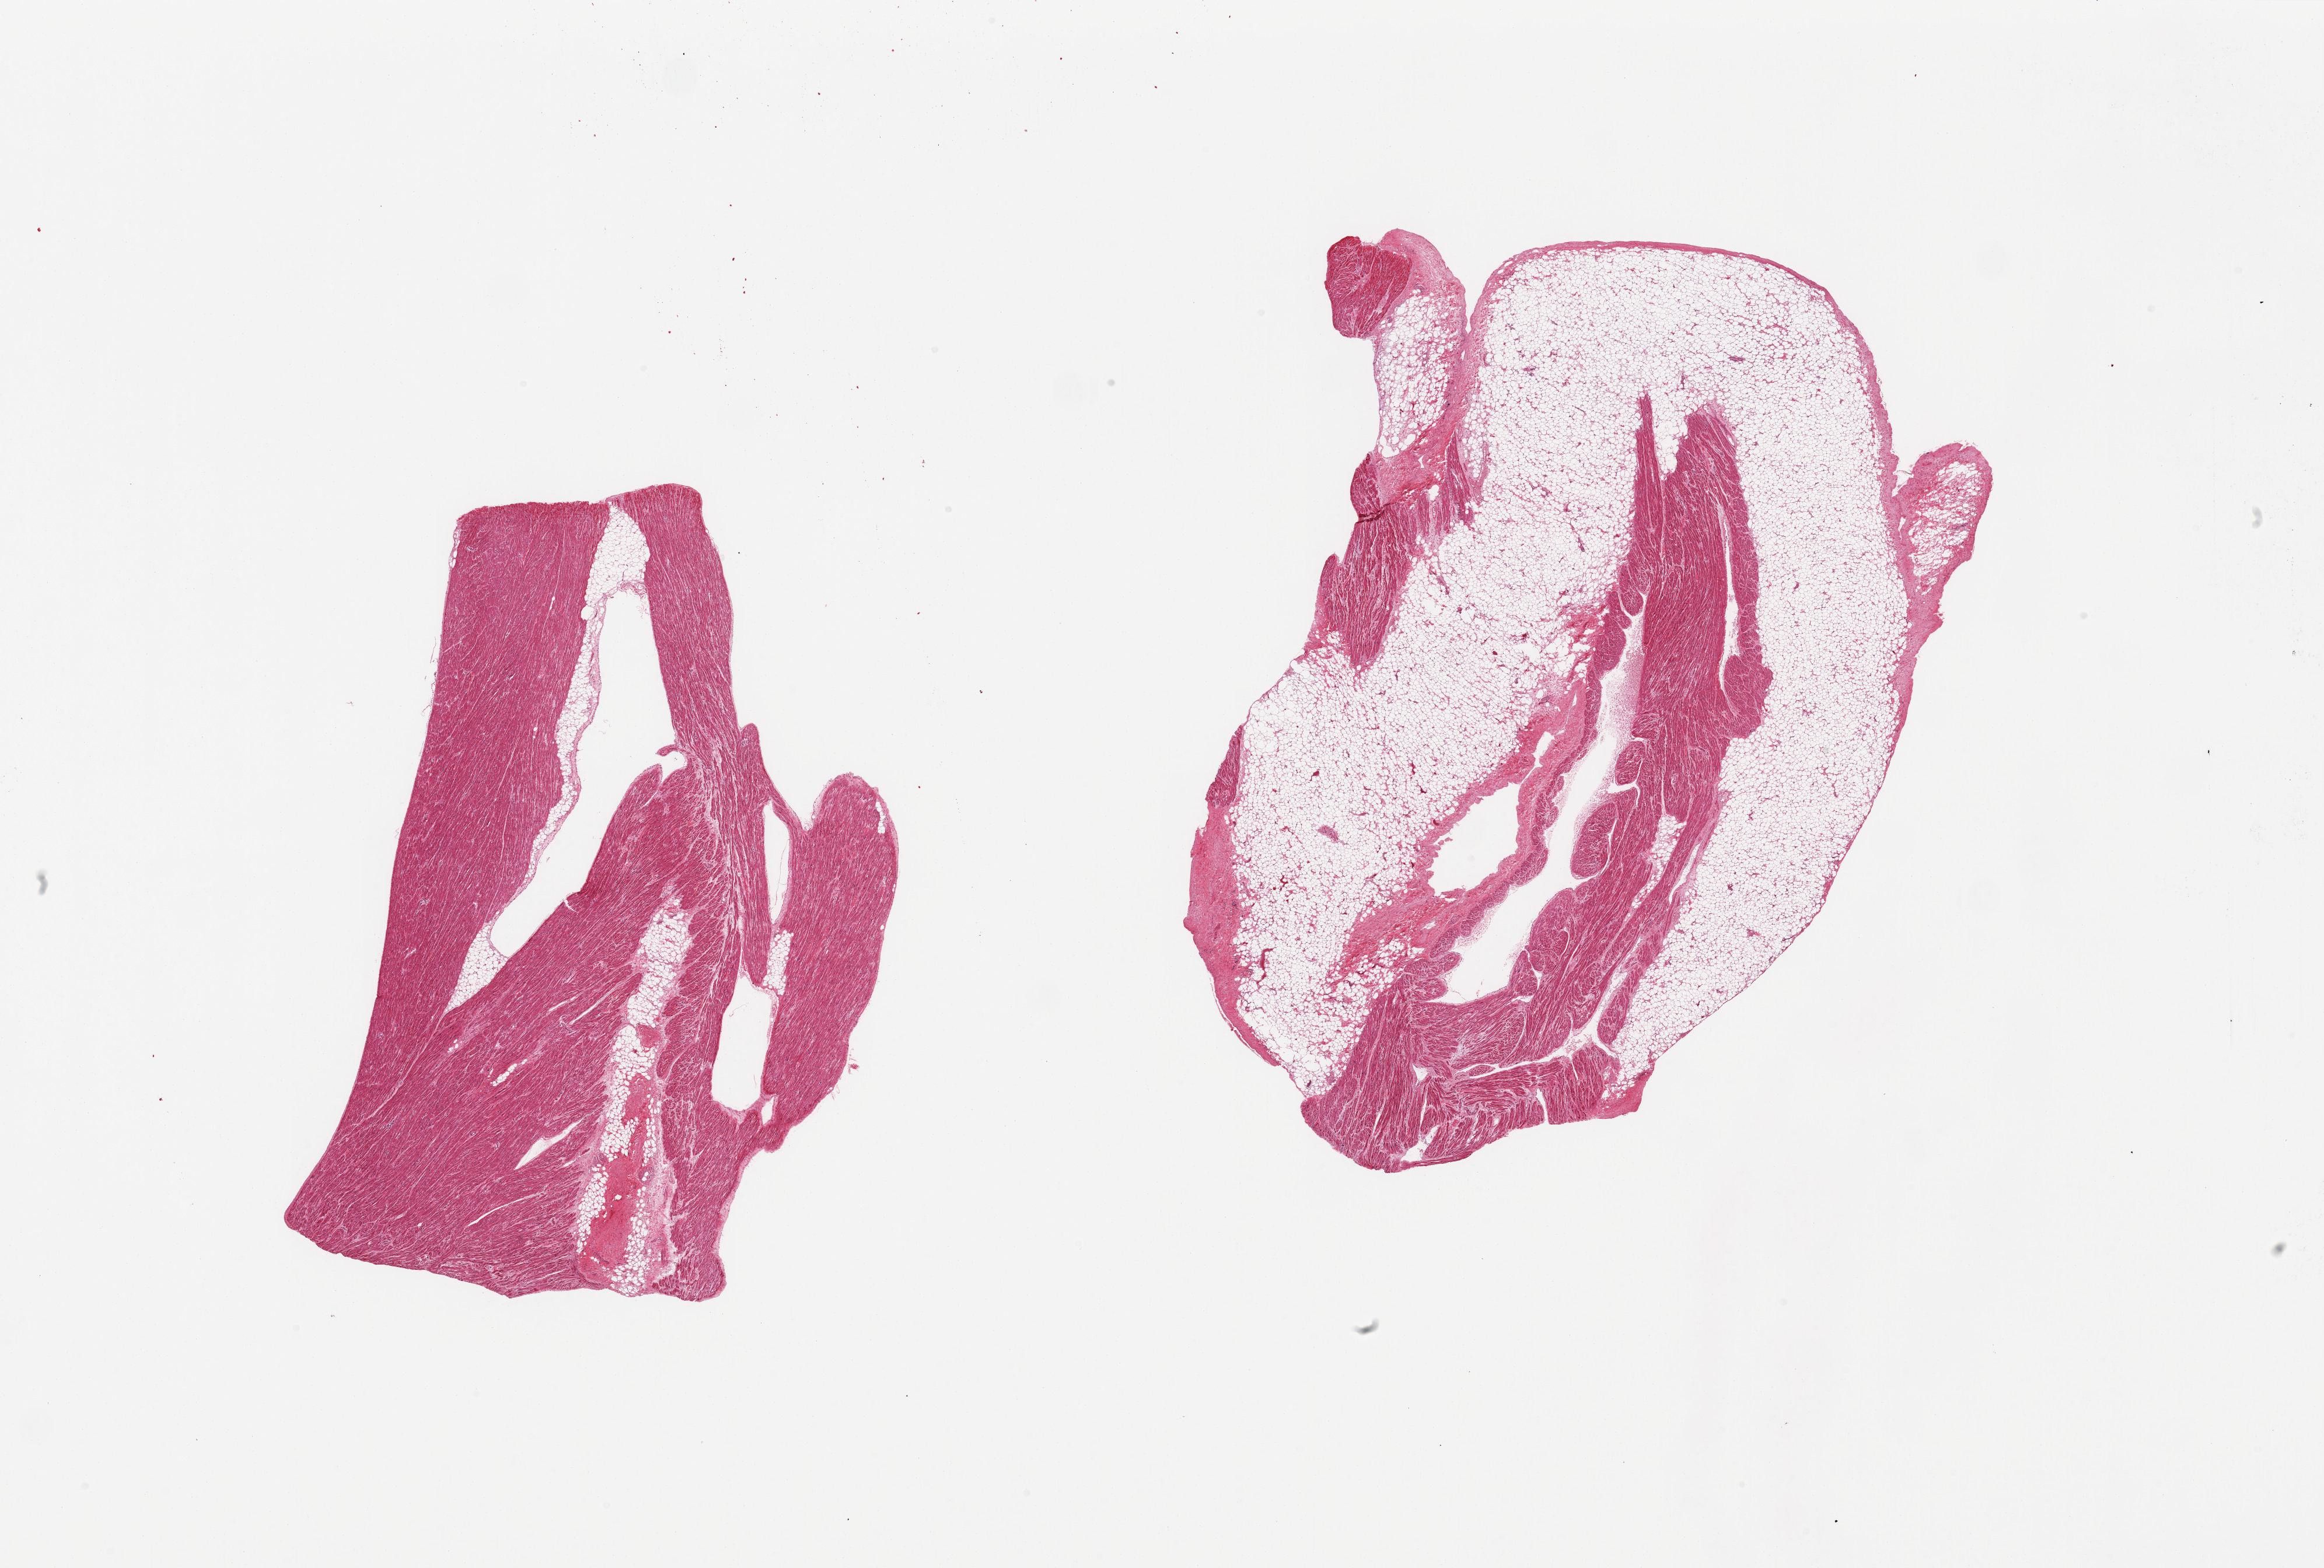
Digitized hematoxylin and eosin (H&E)-stained section, brightfield, whole scanned area (about 31.5 x 21.3 mm, slide scanned at 20x) shown as a low-resolution overview, PAXgene-fixed paraffin-embedded (PFPE) section, target tissue: auricular appendage, donor tissue sample. Female donor.
Pathologist's review note for this sample: 2 pieces; 1 piece is ~60-70% fat.